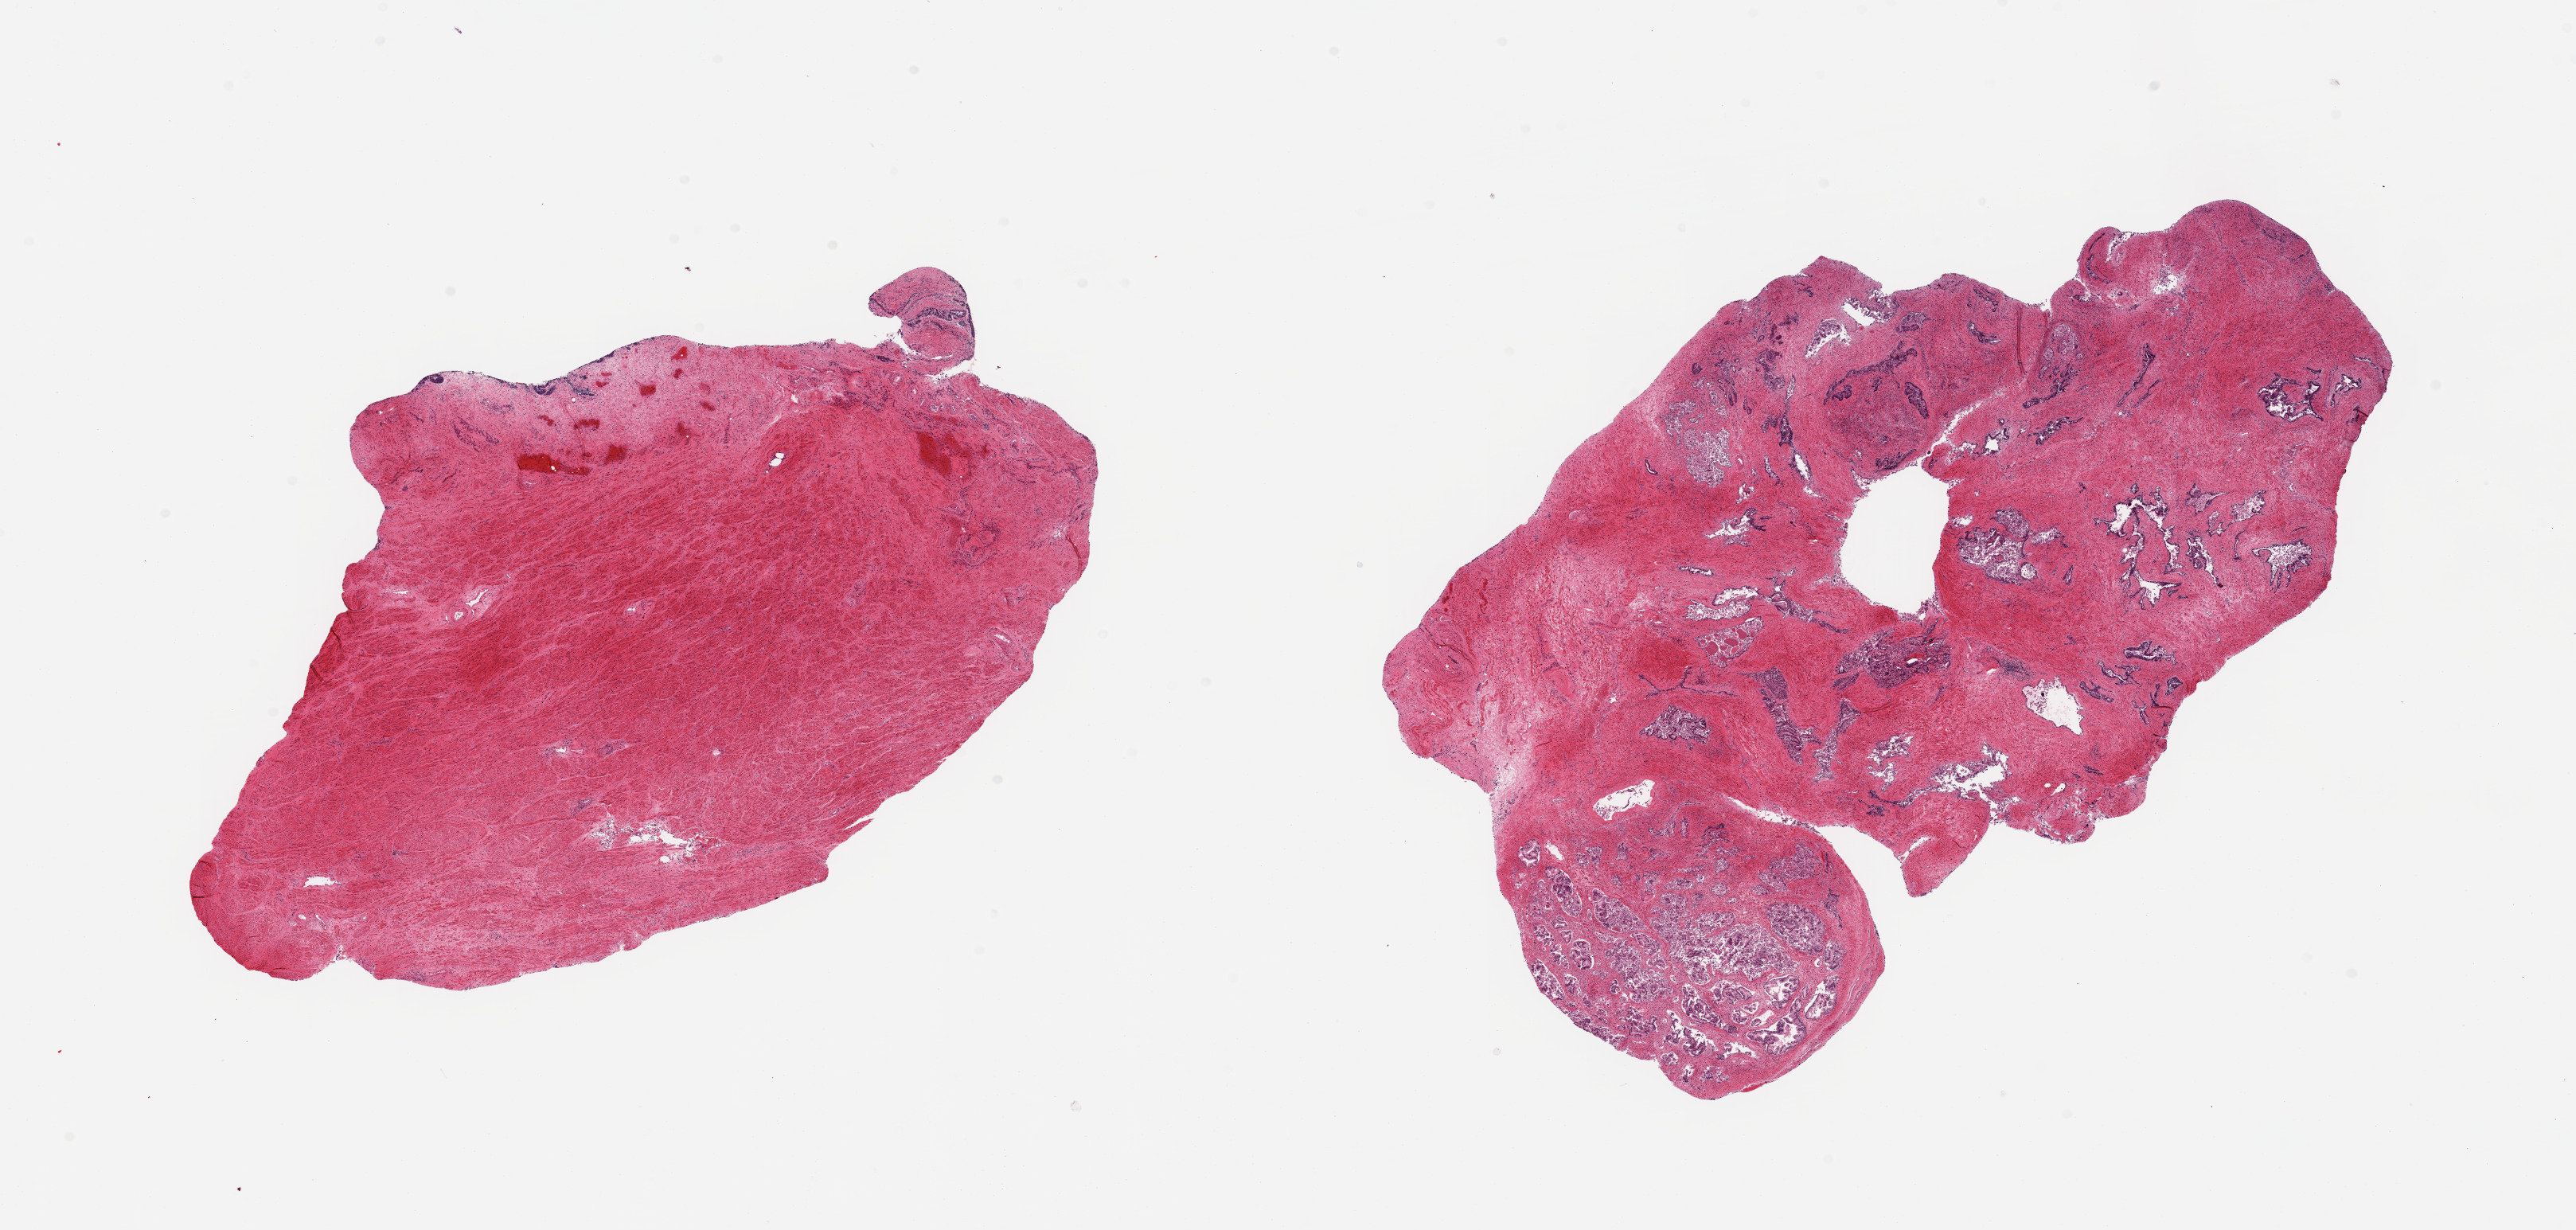
Haematoxylin and eosin whole-slide image, brightfield — a low-resolution overview of the entire scanned area, about 25.6 x 12.2 mm, PAXgene-fixed paraffin-embedded (PFPE) section, target tissue: prostate, tissue donor sample. Male donor.
Reviewer comment on this tissue sample: 2 pieces; glands autolyzed; stroma intact; 1 piece all smooth muscle.